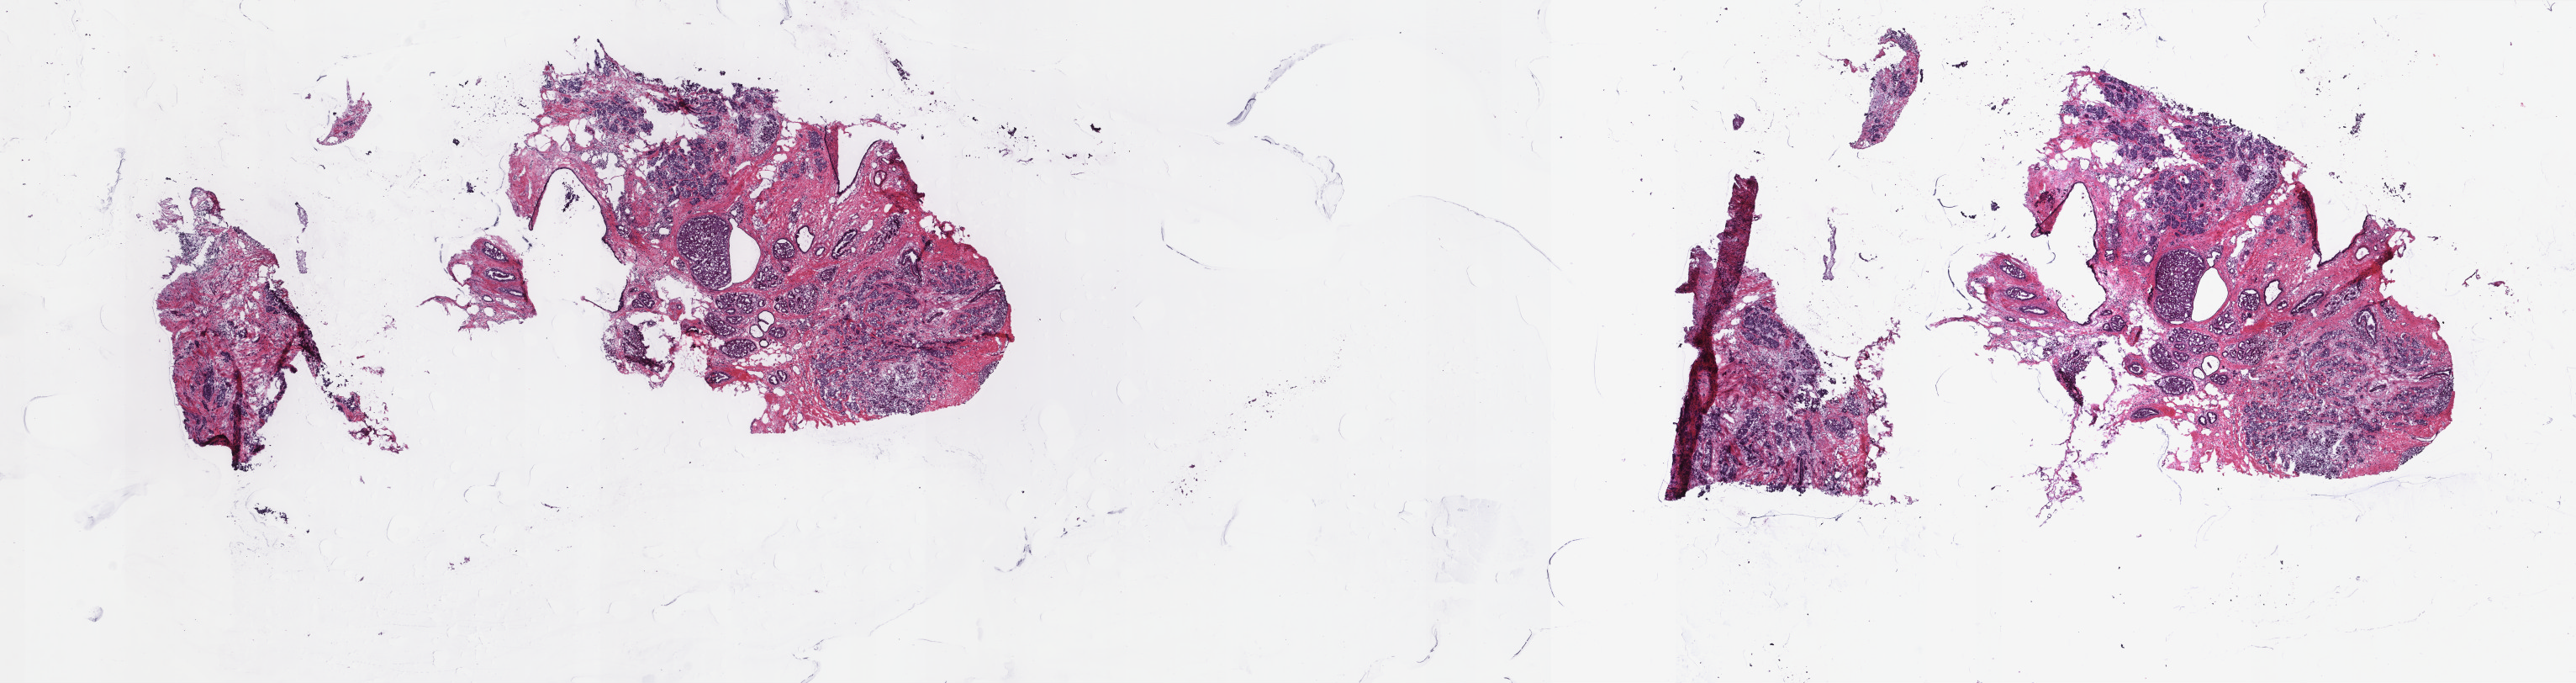
Digitized Hematoxylin and eosin (H&E) stained tissue section (whole slide) — shown as a low-resolution overview of the whole scanned area (about 24.3 x 6.4 mm, from a 40x scan), frozen section from the top of the tissue portion, sample: primary tumour, breast. Female patient; age at initial diagnosis 57 years. Slide review estimates, as recorded: tumour cells 50%, tumour nuclei 65%, normal cells 10%, stromal cells 40%, necrosis 0%. Inflammatory infiltration, as recorded: lymphocyte infiltration 0%, monocyte infiltration 0%, neutrophil infiltration 0%.
* lymph nodes positive (case pathology): 24 of 30 examined
* AJCC pathologic stage: IIIB
* diagnosis: Infiltrating duct carcinoma, NOS